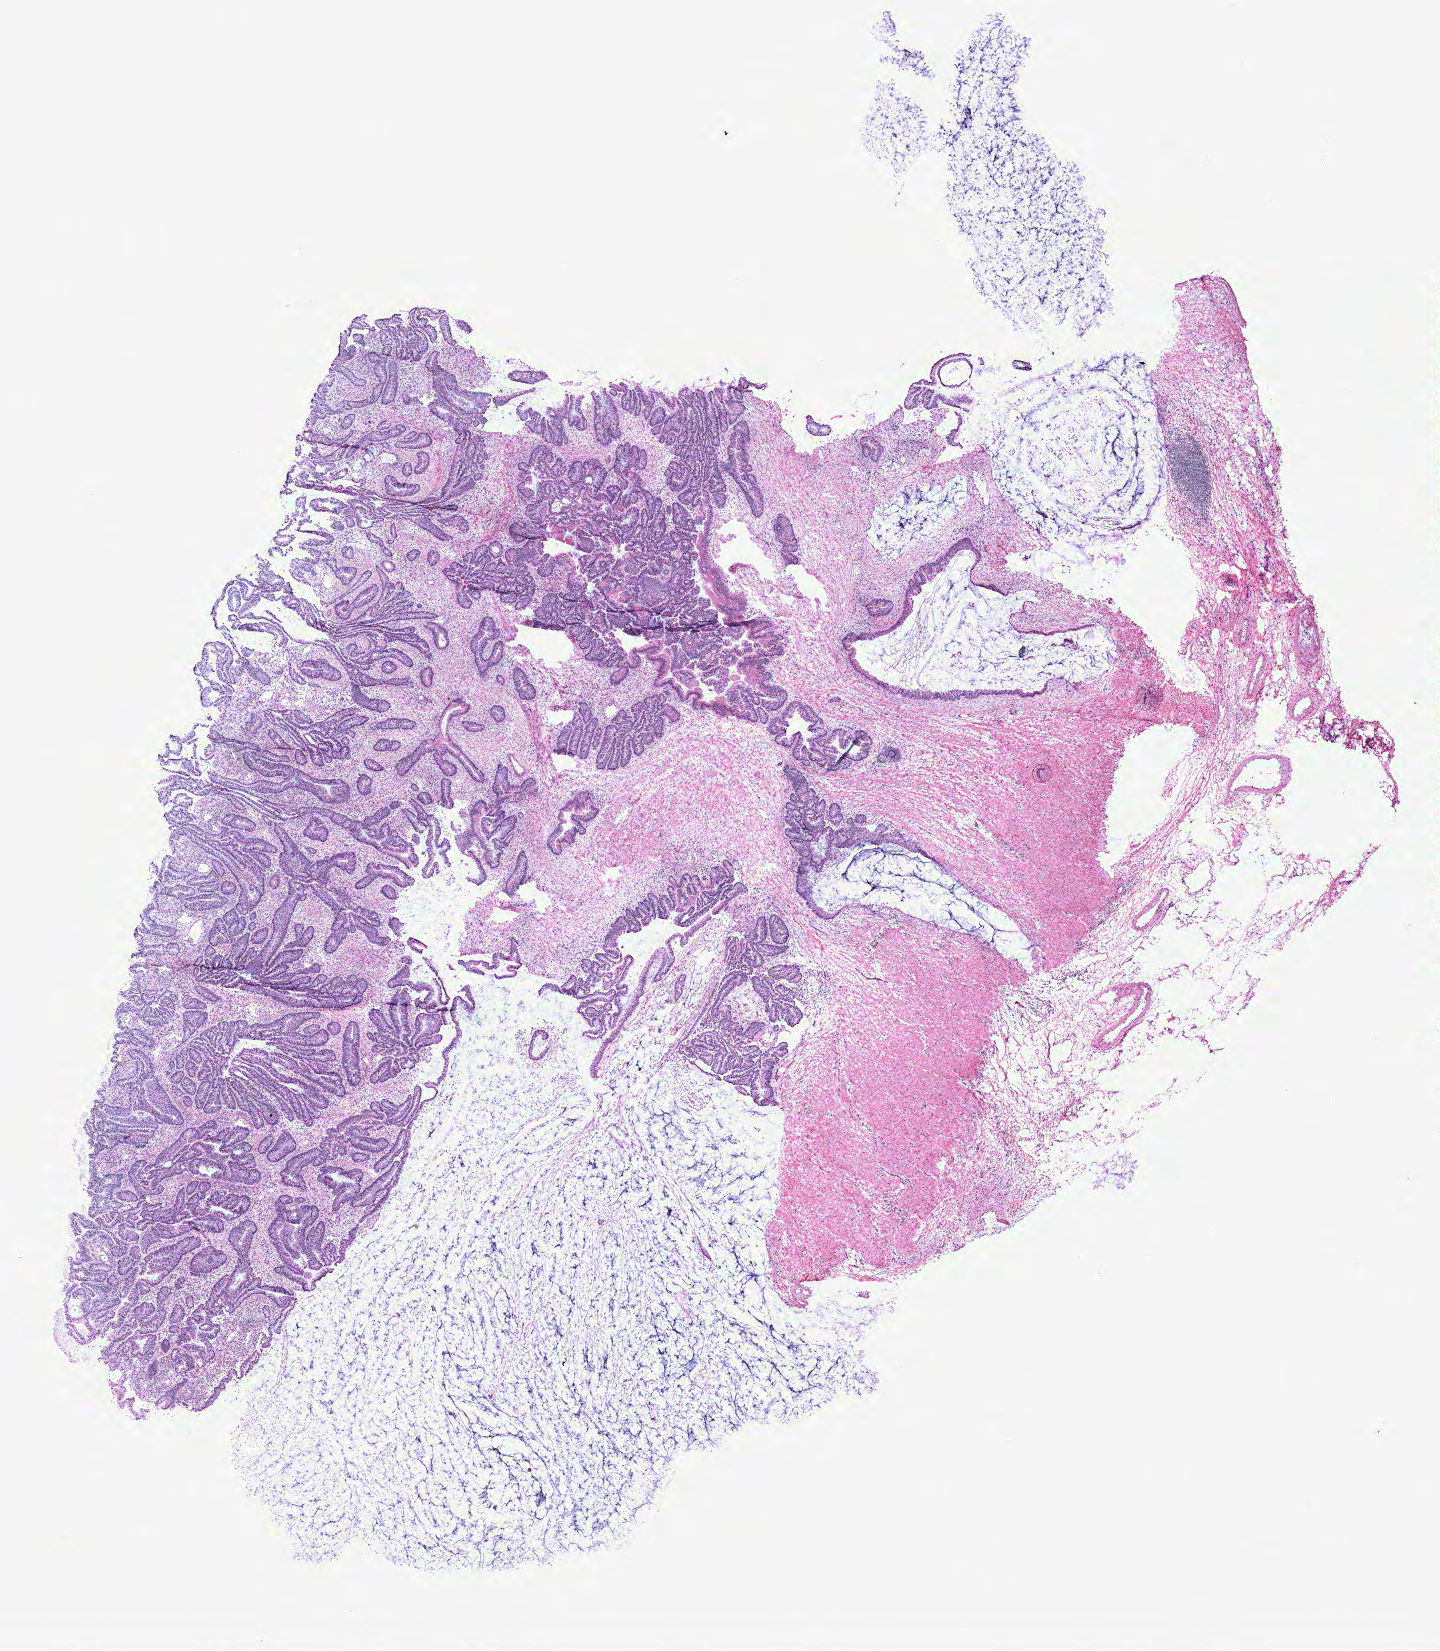
Digitized Hematoxylin and eosin (H&E) stained tissue section (whole slide), whole scanned area (about 11.5 x 13.2 mm) shown as a low-resolution overview, colon, tissue type not recorded.
* patient diagnosis (cohort enrolment): colon cancer (colon)